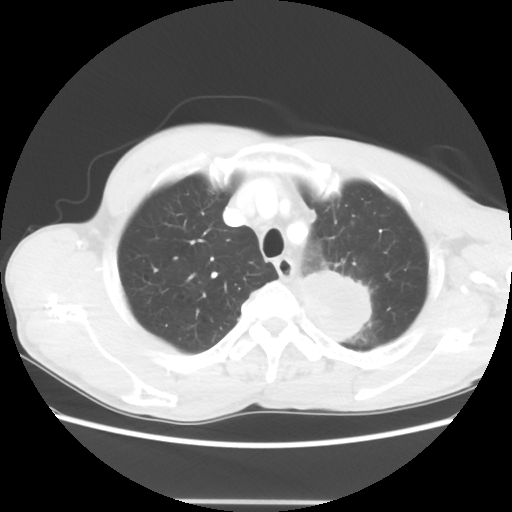
Chest CT, one axial slice. Slice 53 of 62 in the series (ordered by position). Reconstruction kernel STANDARD. 100 kVp. Lung window (W 1500 / L -600 HU). 512 × 512 image matrix, field of view 360 × 360 mm. Male patient, age 61 years. Case-level facts recorded for this patient, not image findings: clinical TNM (as recorded): T3 N1 M1.
Structures marked on this image (rectangle marked by the reading radiologist):
- lung tumour (recorded histology: adenocarcinoma): box from (x=296, y=268) to (x=371, y=345) px